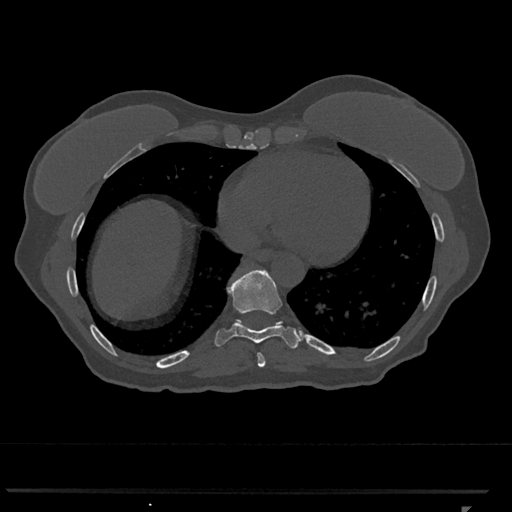
CT including the spine, one axial slice; position 615 of 793 along the scan axis; reconstruction kernel Br40s/3; 120 kVp; bone window (W 1800 / L 400 HU); 0.5 mm slice thickness; 512 × 512 image matrix. Patient: female, 62 years. Case-level facts recorded for this patient, not image findings: primary cancer: renal.
Outlined on this slice (semi-automatically segmented with operator editing):
- T10 vertebra: bounding box (x1, y1, x2, y2) in pixels: (241, 321, 281, 325)
- T8 vertebra: (257, 353, 266, 367)
- T9 vertebra: (214, 270, 300, 349)